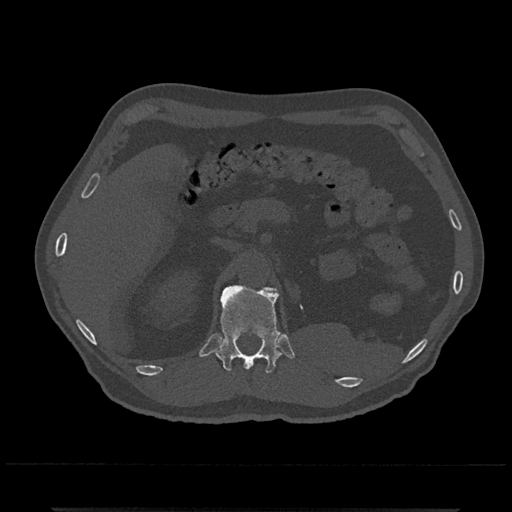
CT including the spine, one axial slice; position 430 of 797 along the scan axis; reconstruction kernel Br40s/3; bone window (W 1800 / L 400 HU); 0.5 mm slice thickness; 512 × 512 image matrix. Male patient, age 67 years. From the clinical record (not read from this slice): primary cancer: prostate.
Annotated regions visible in this slice (semi-automatically segmented with operator editing):
- T12 vertebra: bounding box [x1, y1, x2, y2] px = [214, 285, 282, 373]